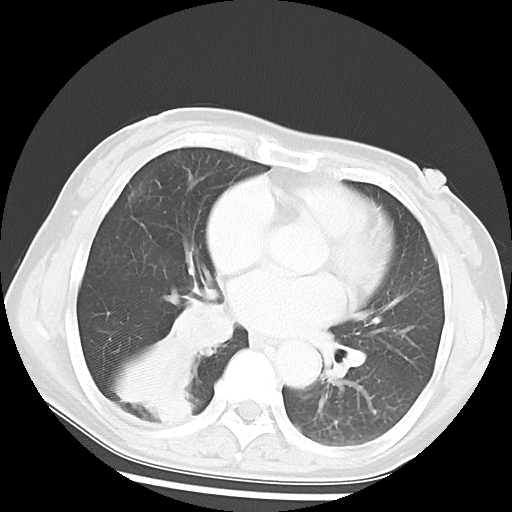
Chest CT, one axial slice; position 26 of 52 along the scan axis; reconstruction kernel LUNG; lung window (W 1500 / L -600 HU); 5 mm slice thickness; 512 × 512 image matrix, field of view 297 × 297 mm. Female patient, age 54 years. From the clinical record (not read from this slice): clinical TNM (as recorded): T1c N0 M0.
Structures marked on this image (rectangle marked by the reading radiologist):
- lung tumour (recorded histology: squamous cell carcinoma): bounding box <170,293,237,365> (left, top, right, bottom; pixels)